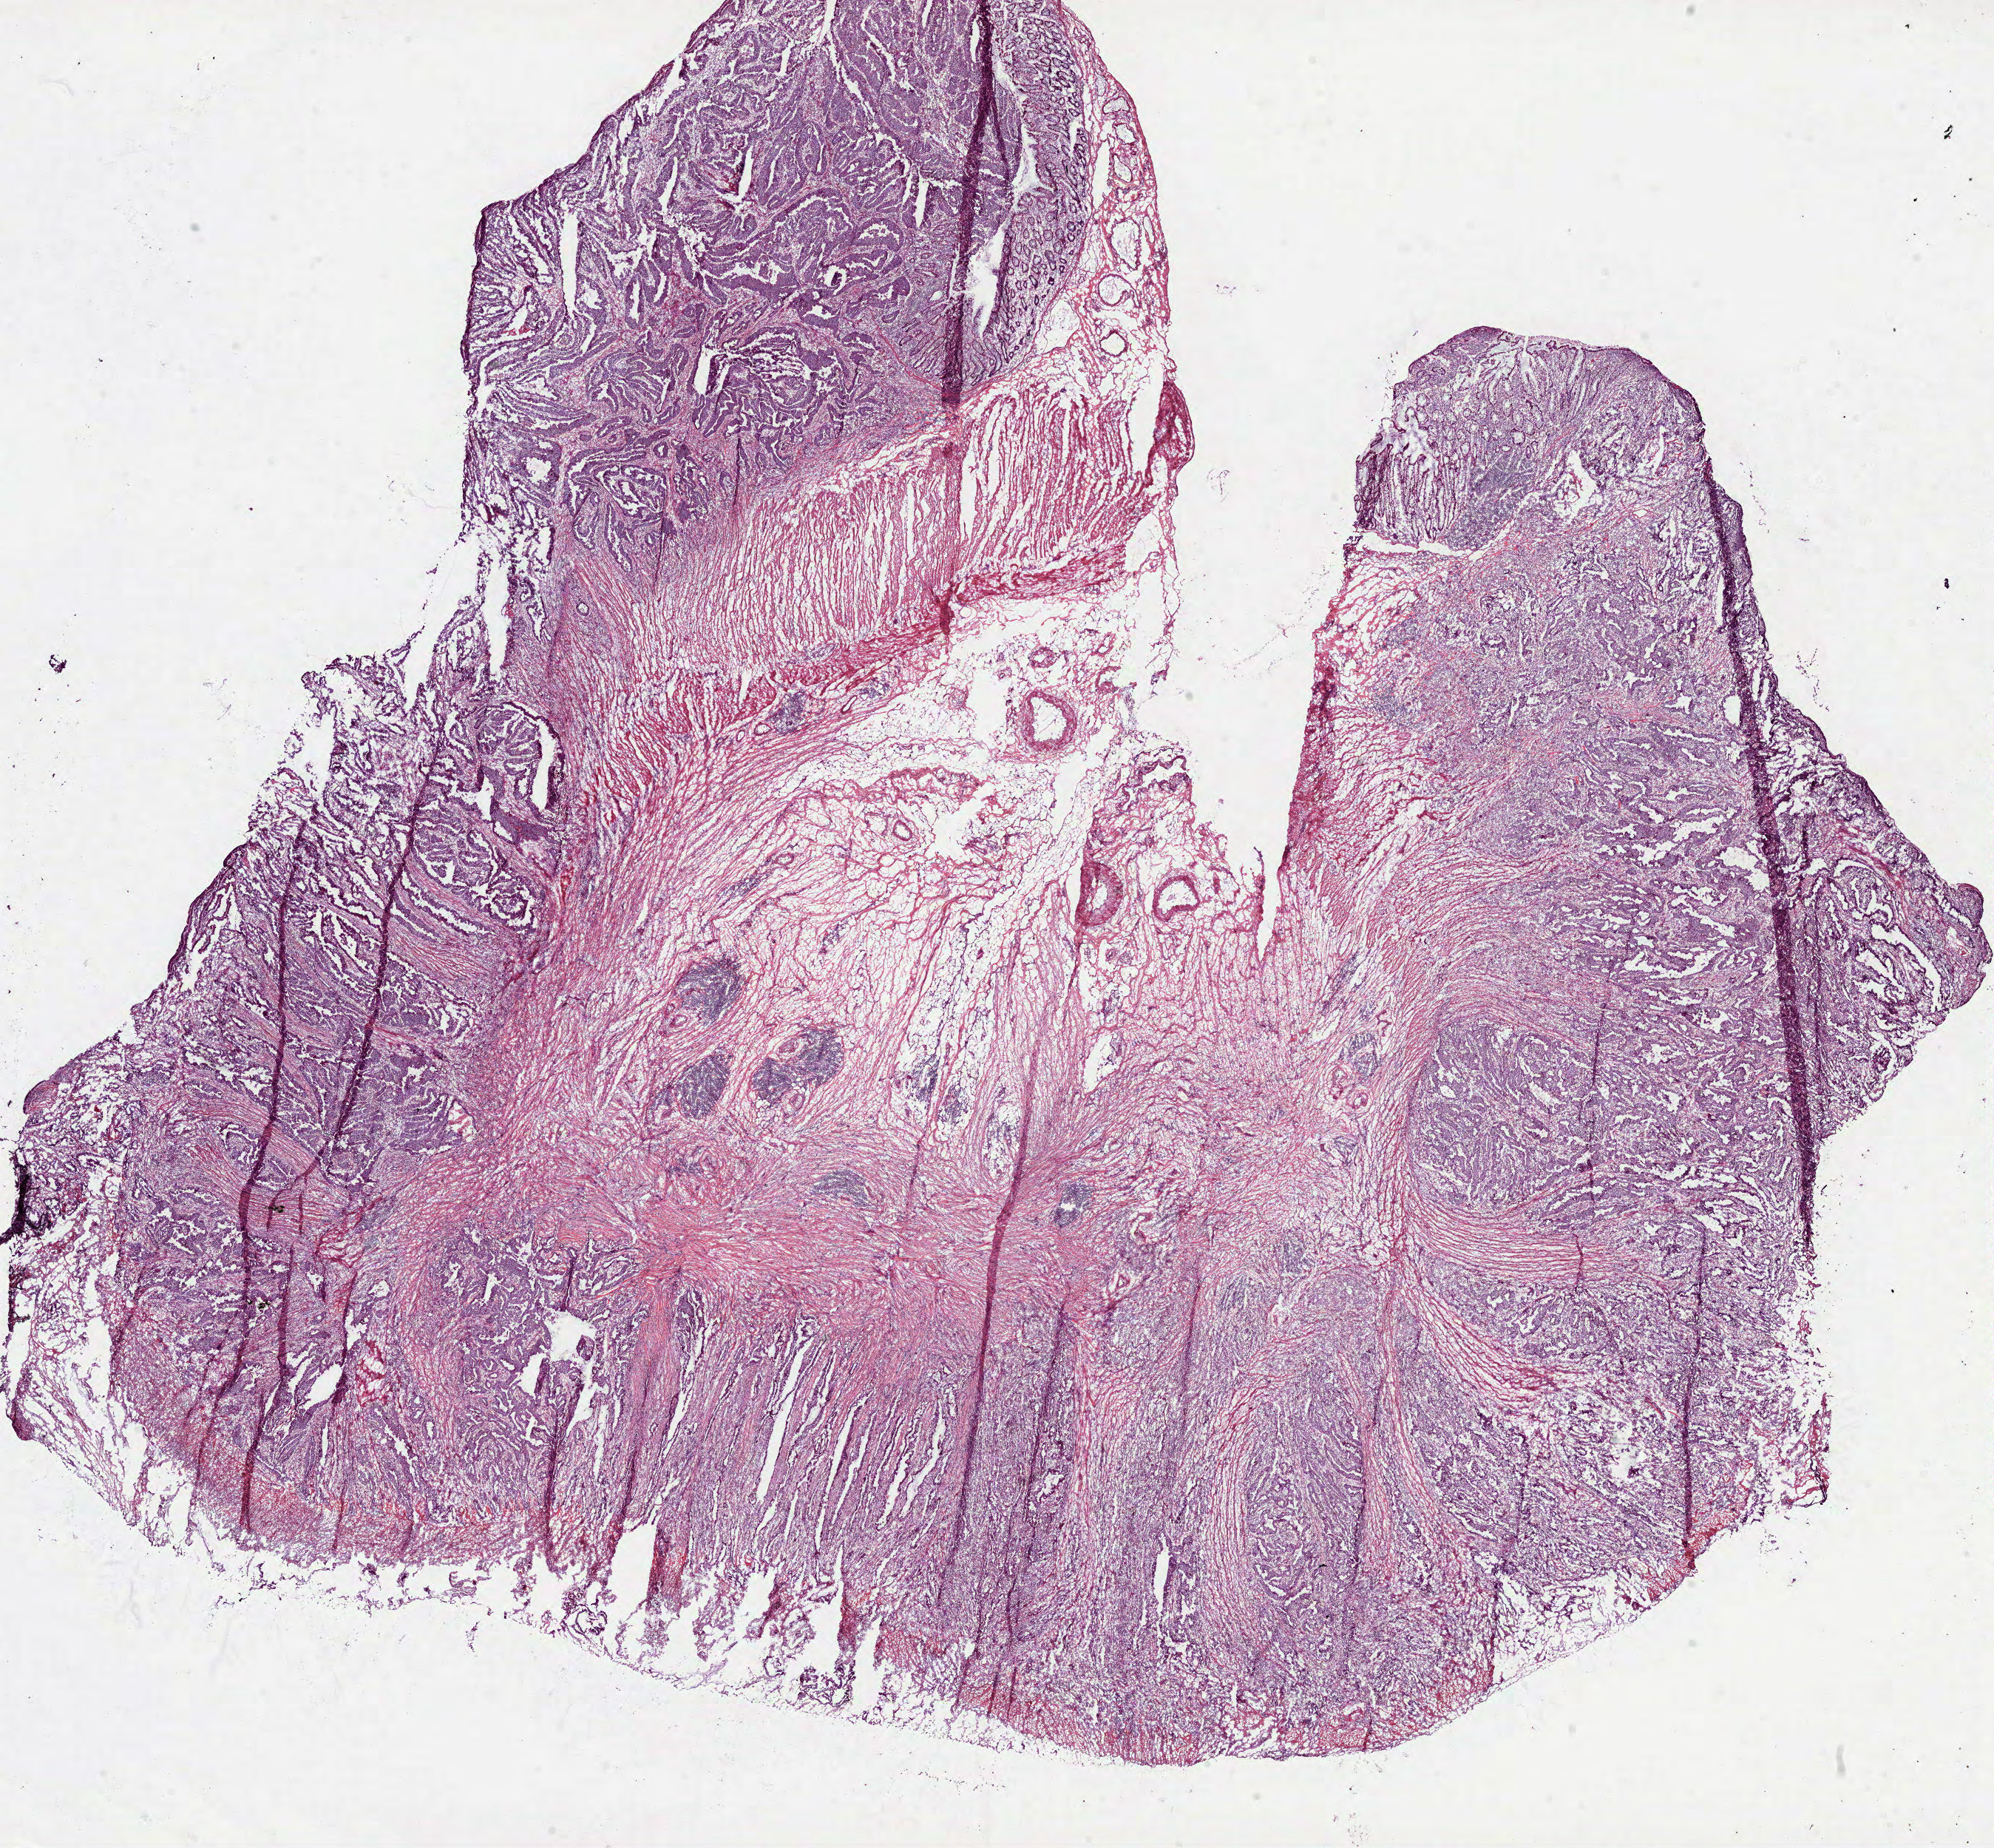
Whole-slide histology image, H&E-stained, low-resolution overview of the scanned area, about 21.8 x 20.2 mm (slide scanned at 40x); frozen section; sample: primary tumour, colon. Female patient; age at initial diagnosis 51 years. Composition of this section per pathologist review: tumour cells 60%, tumour nuclei 80%.
Pathologic diagnosis: Adenocarcinoma, NOS.